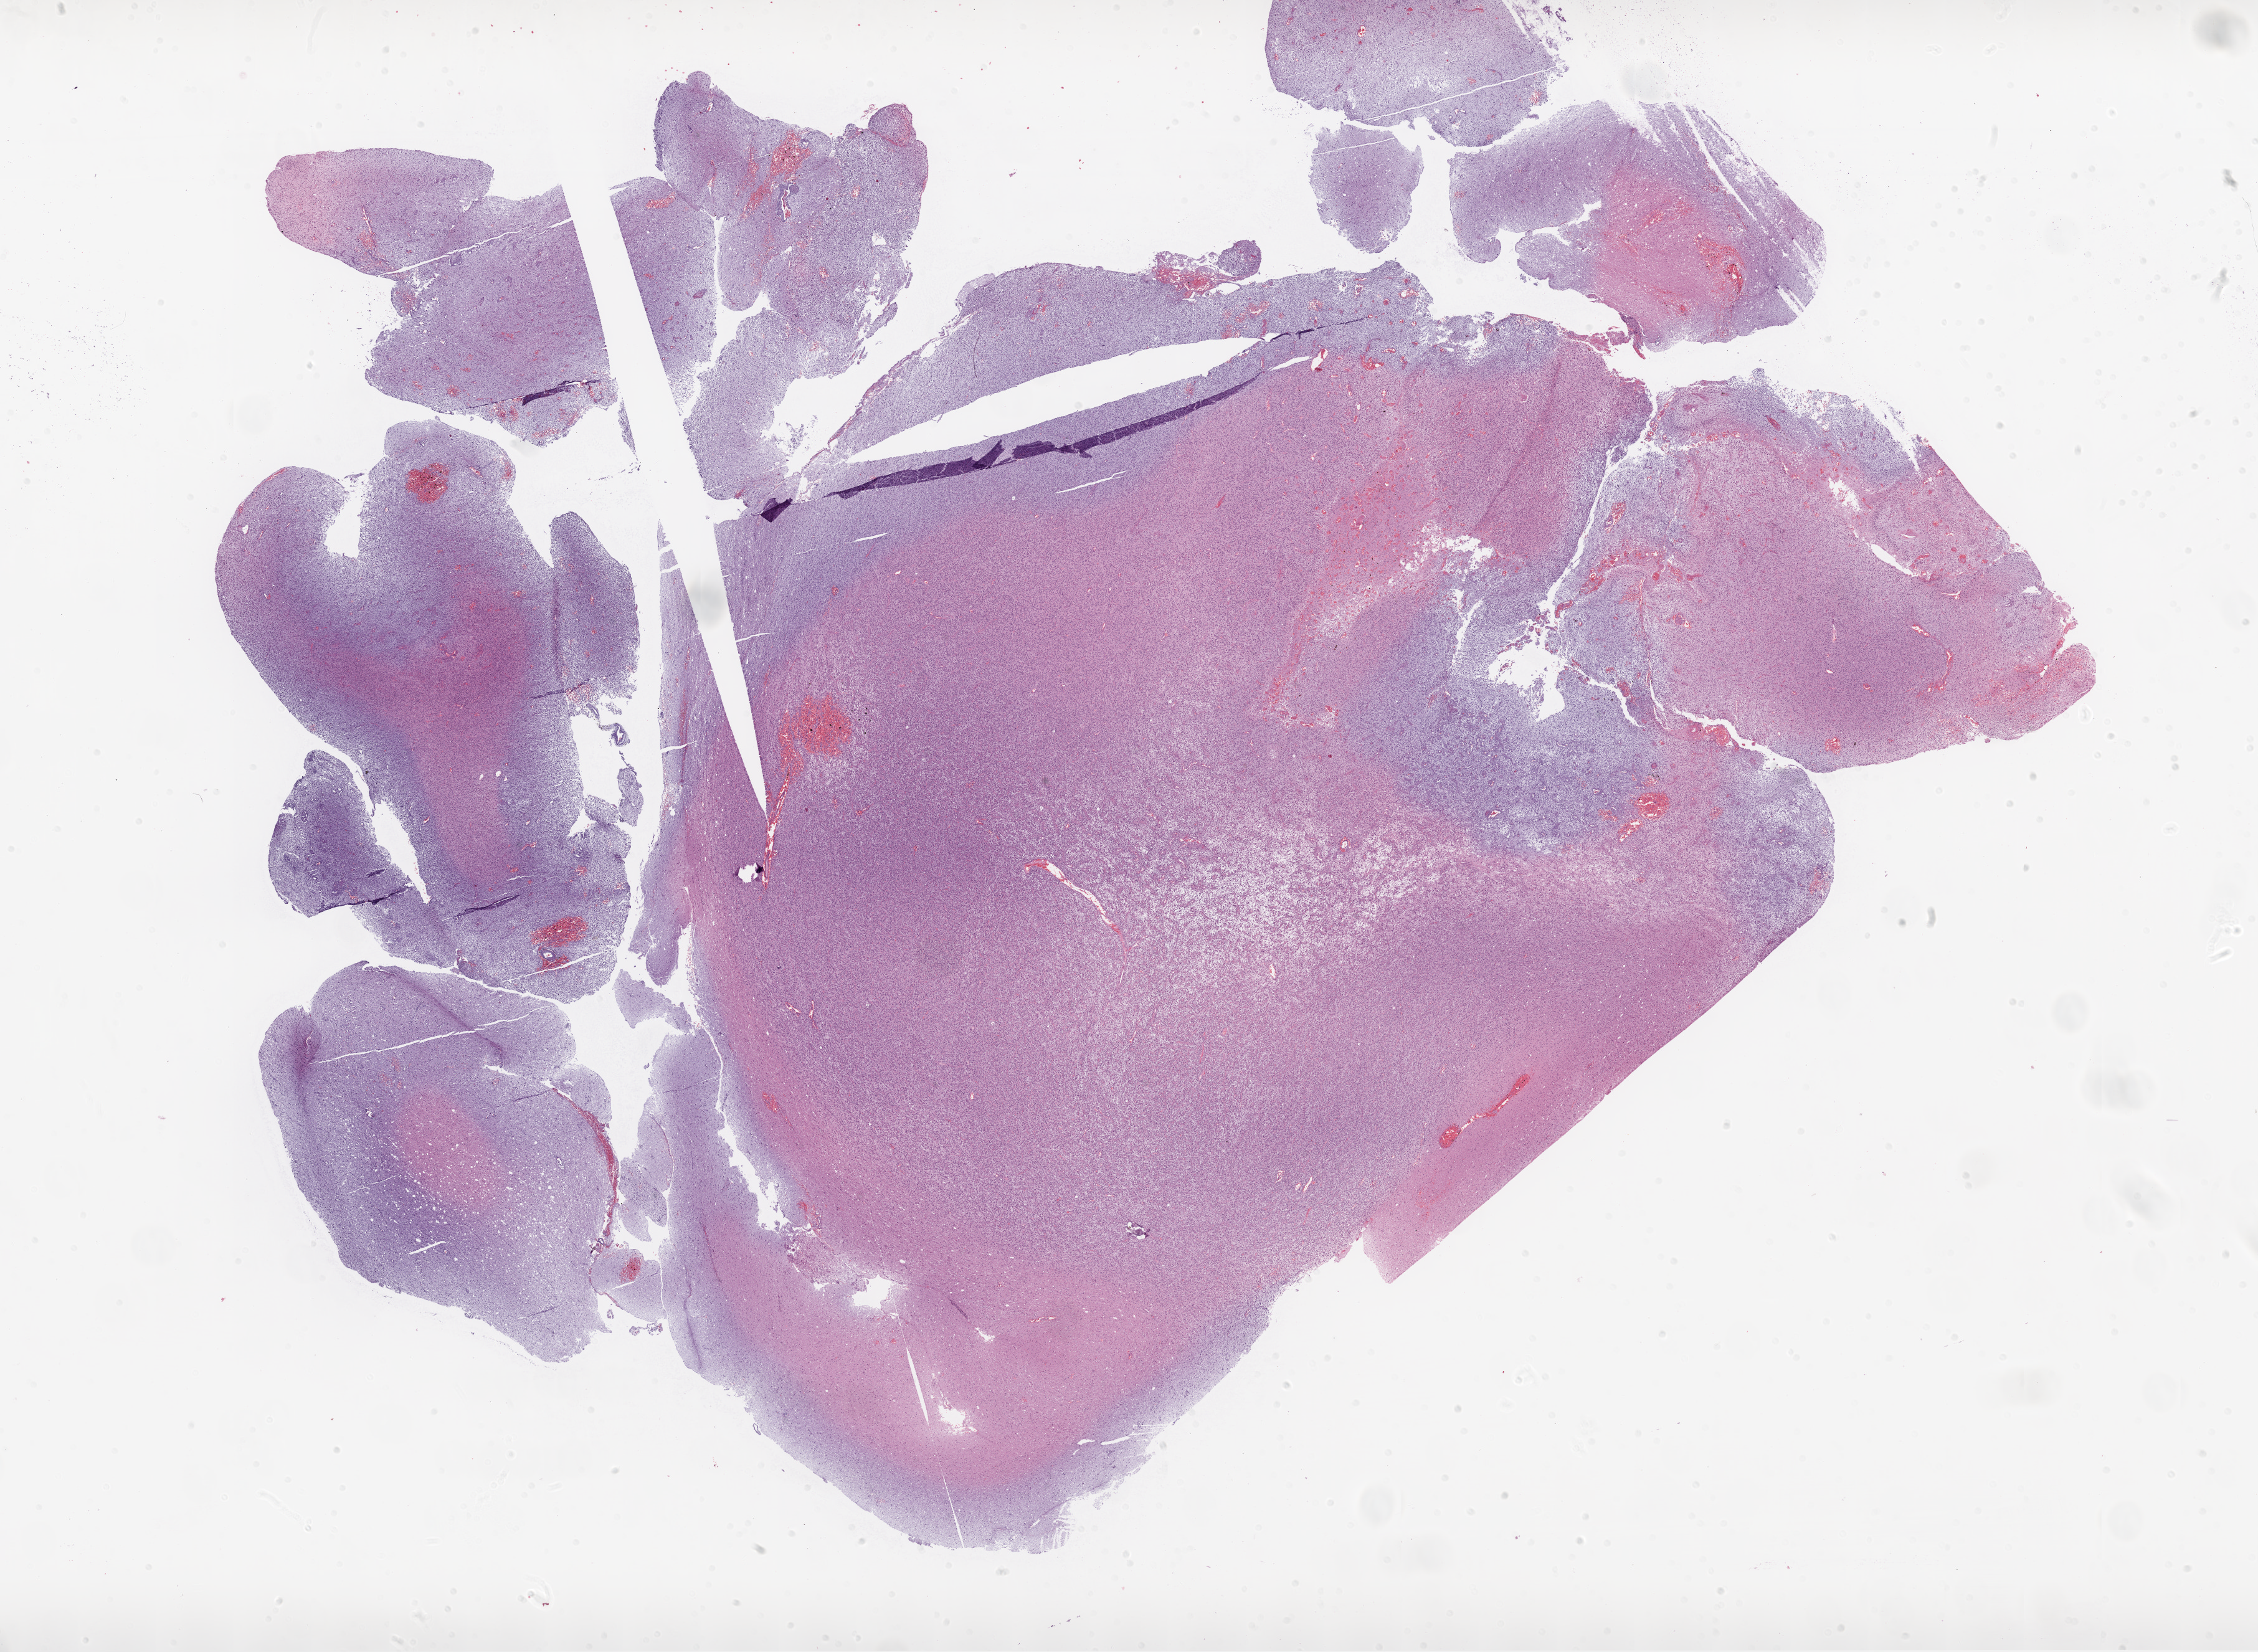
Digitized H&E tissue section (whole slide), whole scanned area (about 29.1 x 21.3 mm, slide scanned at 20x) shown as a low-resolution overview, FFPE section, brain, primary tumour sample. Patient: female, age at initial diagnosis 67 years.
Histologic diagnosis: Glioblastoma.